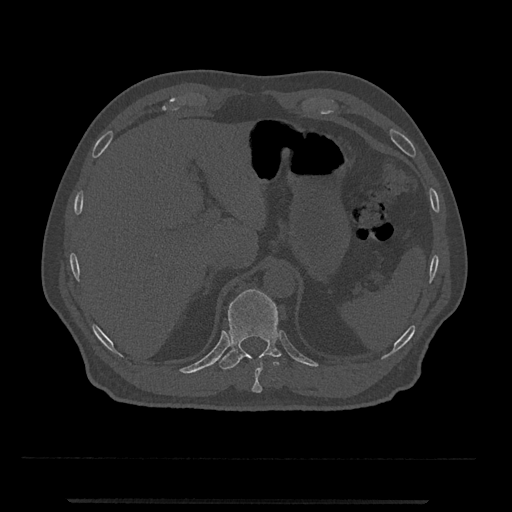
CT including the spine, one axial slice. Slice 480 of 797 in the series (ordered by position). Bone window (W 1800 / L 400 HU). 0.5 mm slice thickness. 512 × 512 image matrix. Patient: male, 63 years. Case-level facts recorded for this patient, not image findings: primary cancer: prostate.
Structures marked on this image (semi-automatic segmentation, software-assisted and operator-edited):
- T10 vertebra: box from (x=252, y=355) to (x=277, y=393) px
- T11 vertebra: (x=218, y=289)–(x=282, y=370)